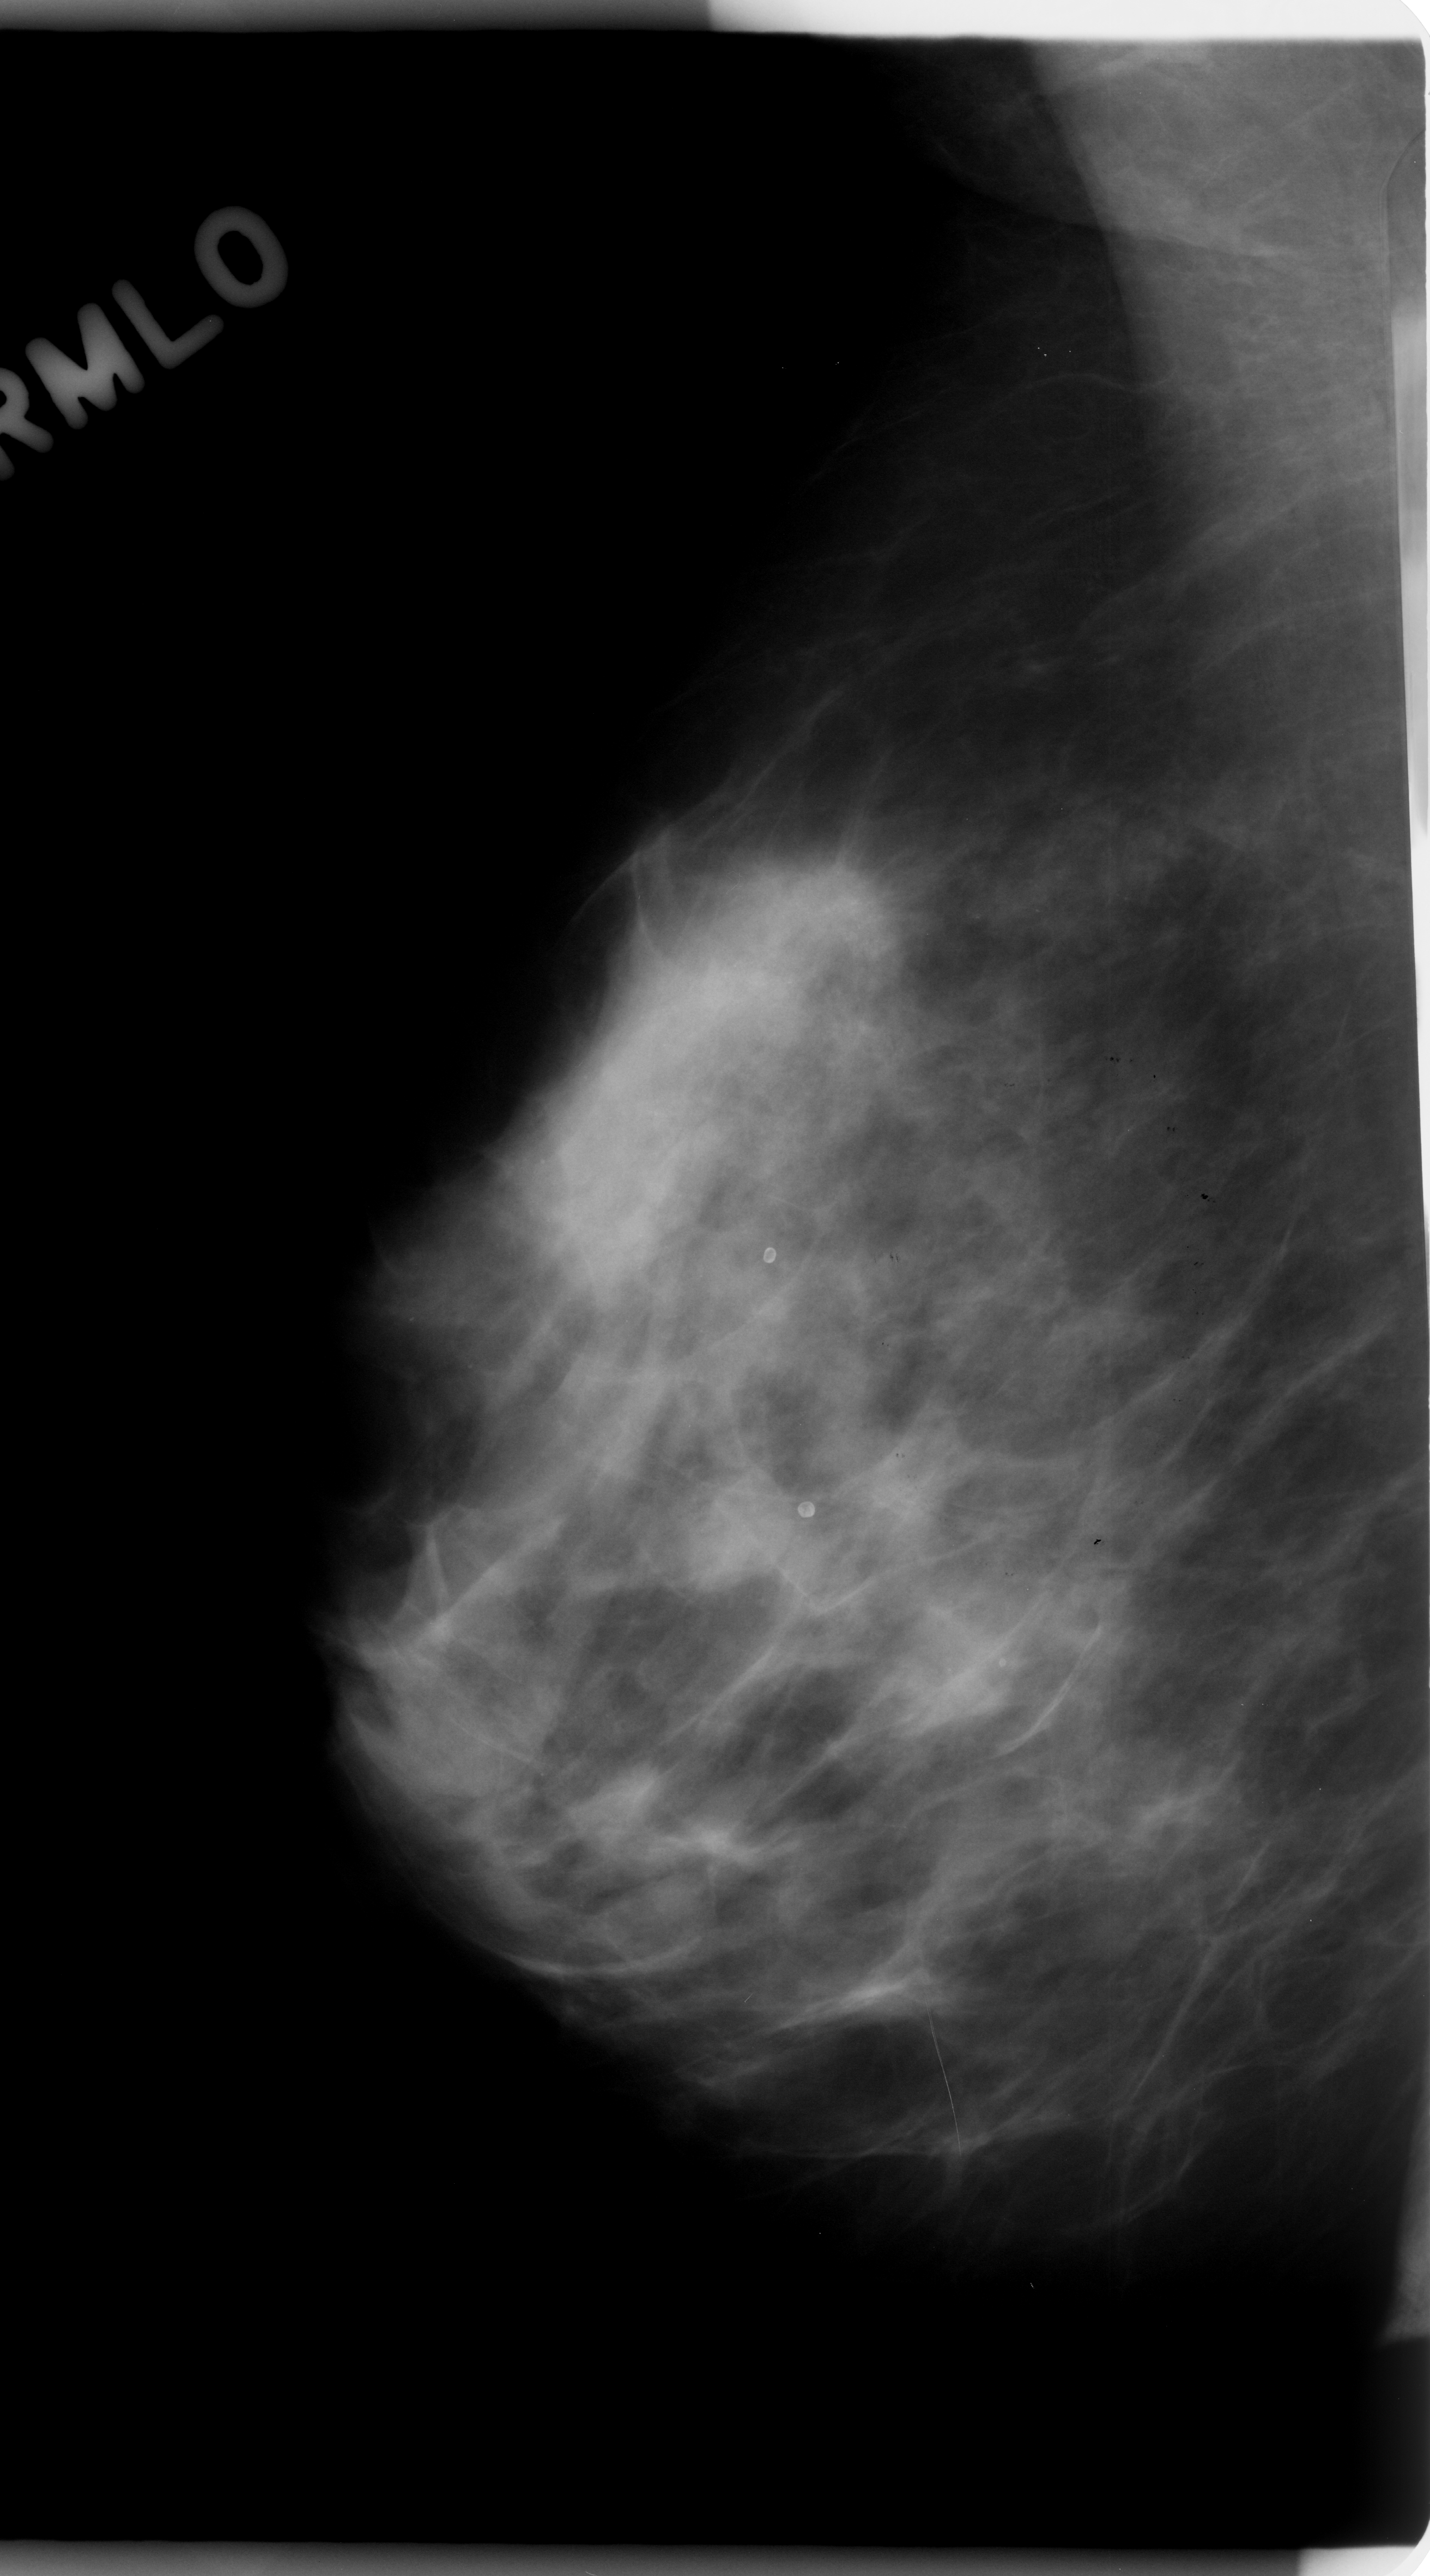
Scanned film-screen mammogram. Right breast. Mediolateral oblique (MLO) view. BI-RADS breast density category 3 (scale 1–4). 1430 × 2576 image matrix.
Expert-marked regions of interest on this image (one box per marked abnormality):
- calcifications, morphology amorphous, distribution clustered; BI-RADS assessment category 5; pathology (as recorded): malignant: bounding box (x1, y1, x2, y2) in pixels: (592, 749, 1026, 1235)